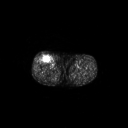
FDG PET of an extremity soft-tissue mass (from a PET/CT study), one axial slice; slice 267 of 311 in the series (ordered by position); 3.27 mm slice thickness; 128 × 128 image matrix, field of view 700 × 700 mm. Male patient, age 56 years. From the clinical record (not read from this slice): histological type: pleiomorphic leiomyosarcoma; grade: intermediate; site of the primary tumour: right thigh.
Structures marked on this image (expert contour drawn on MRI and transferred to this co-registered scan by the dataset authors):
- gross tumour volume including surrounding oedema: bounding box [x1, y1, x2, y2] px = [40, 54, 51, 62]
- gross tumour volume (mass): [41, 56, 50, 62]